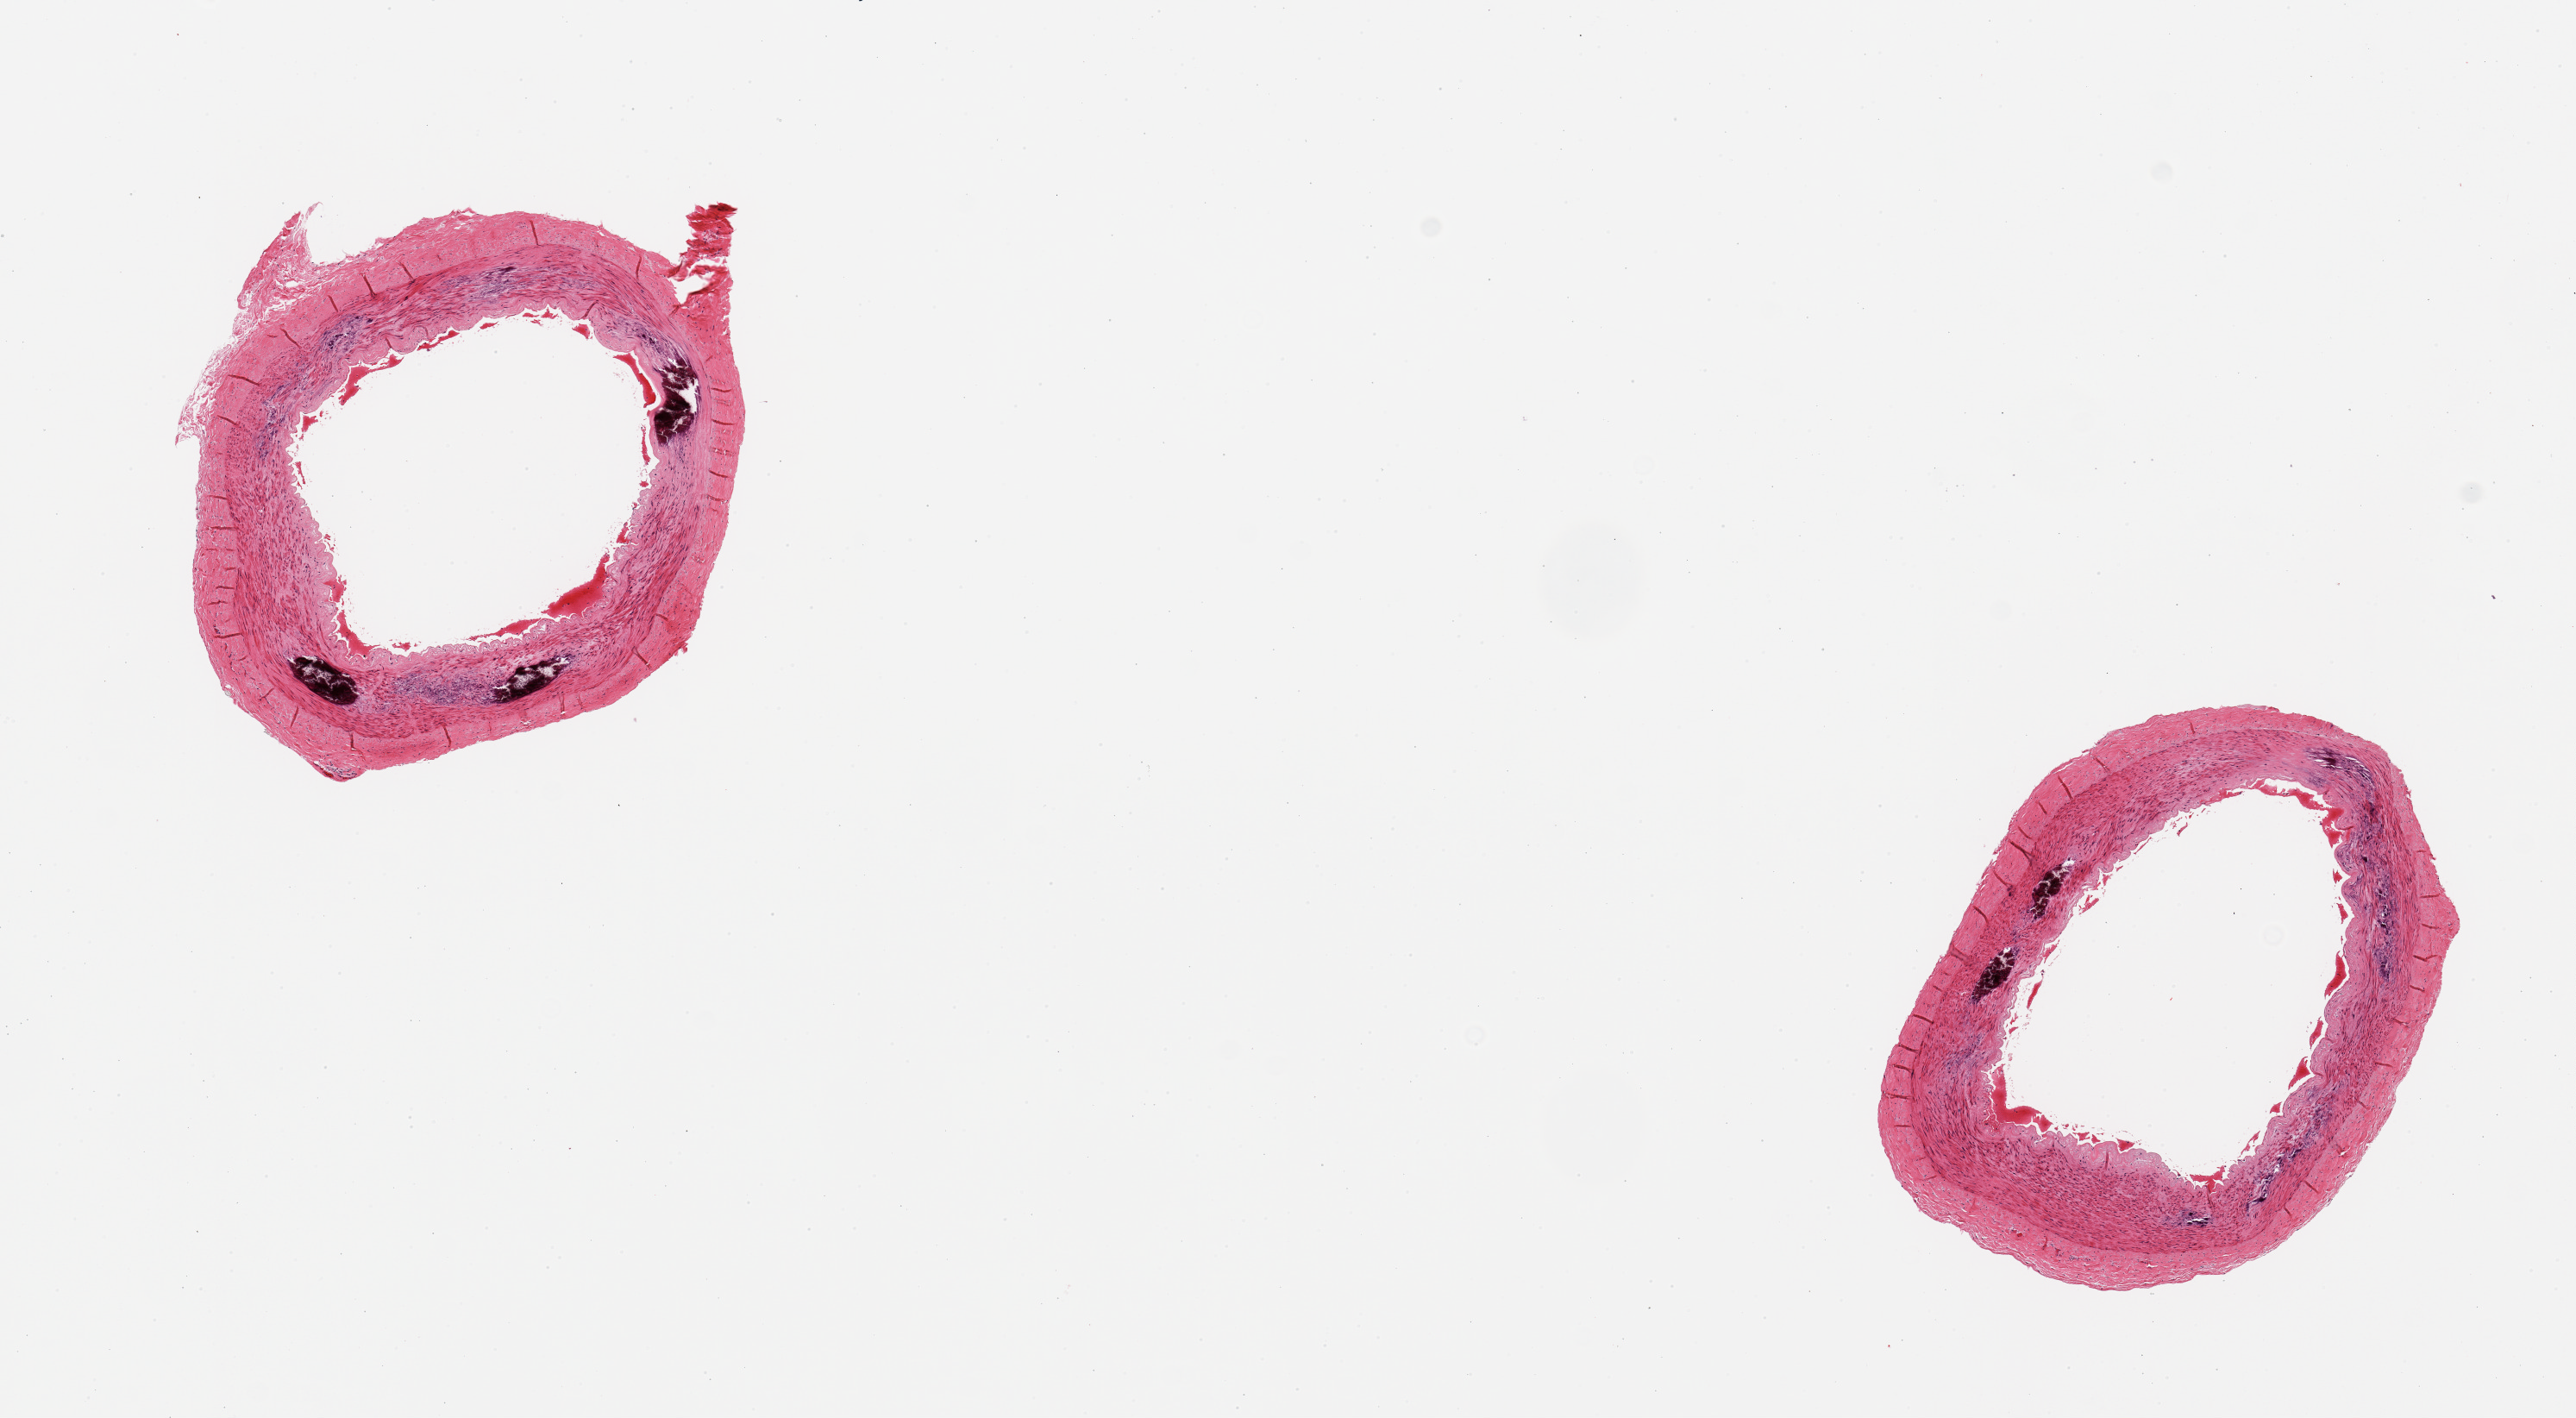
Whole-slide image, haematoxylin and eosin stain — shown as a low-resolution overview of the whole scanned area (about 11.8 x 6.5 mm, acquisition: 20x scan); PAXgene-fixed, paraffin-embedded tissue; sampled site (target tissue): tibial artery; tissue donor sample. Donor sex: female.
Reviewer comment on this tissue sample: 2 pieces; foci of medial calcification; no plaques; well trimmed.